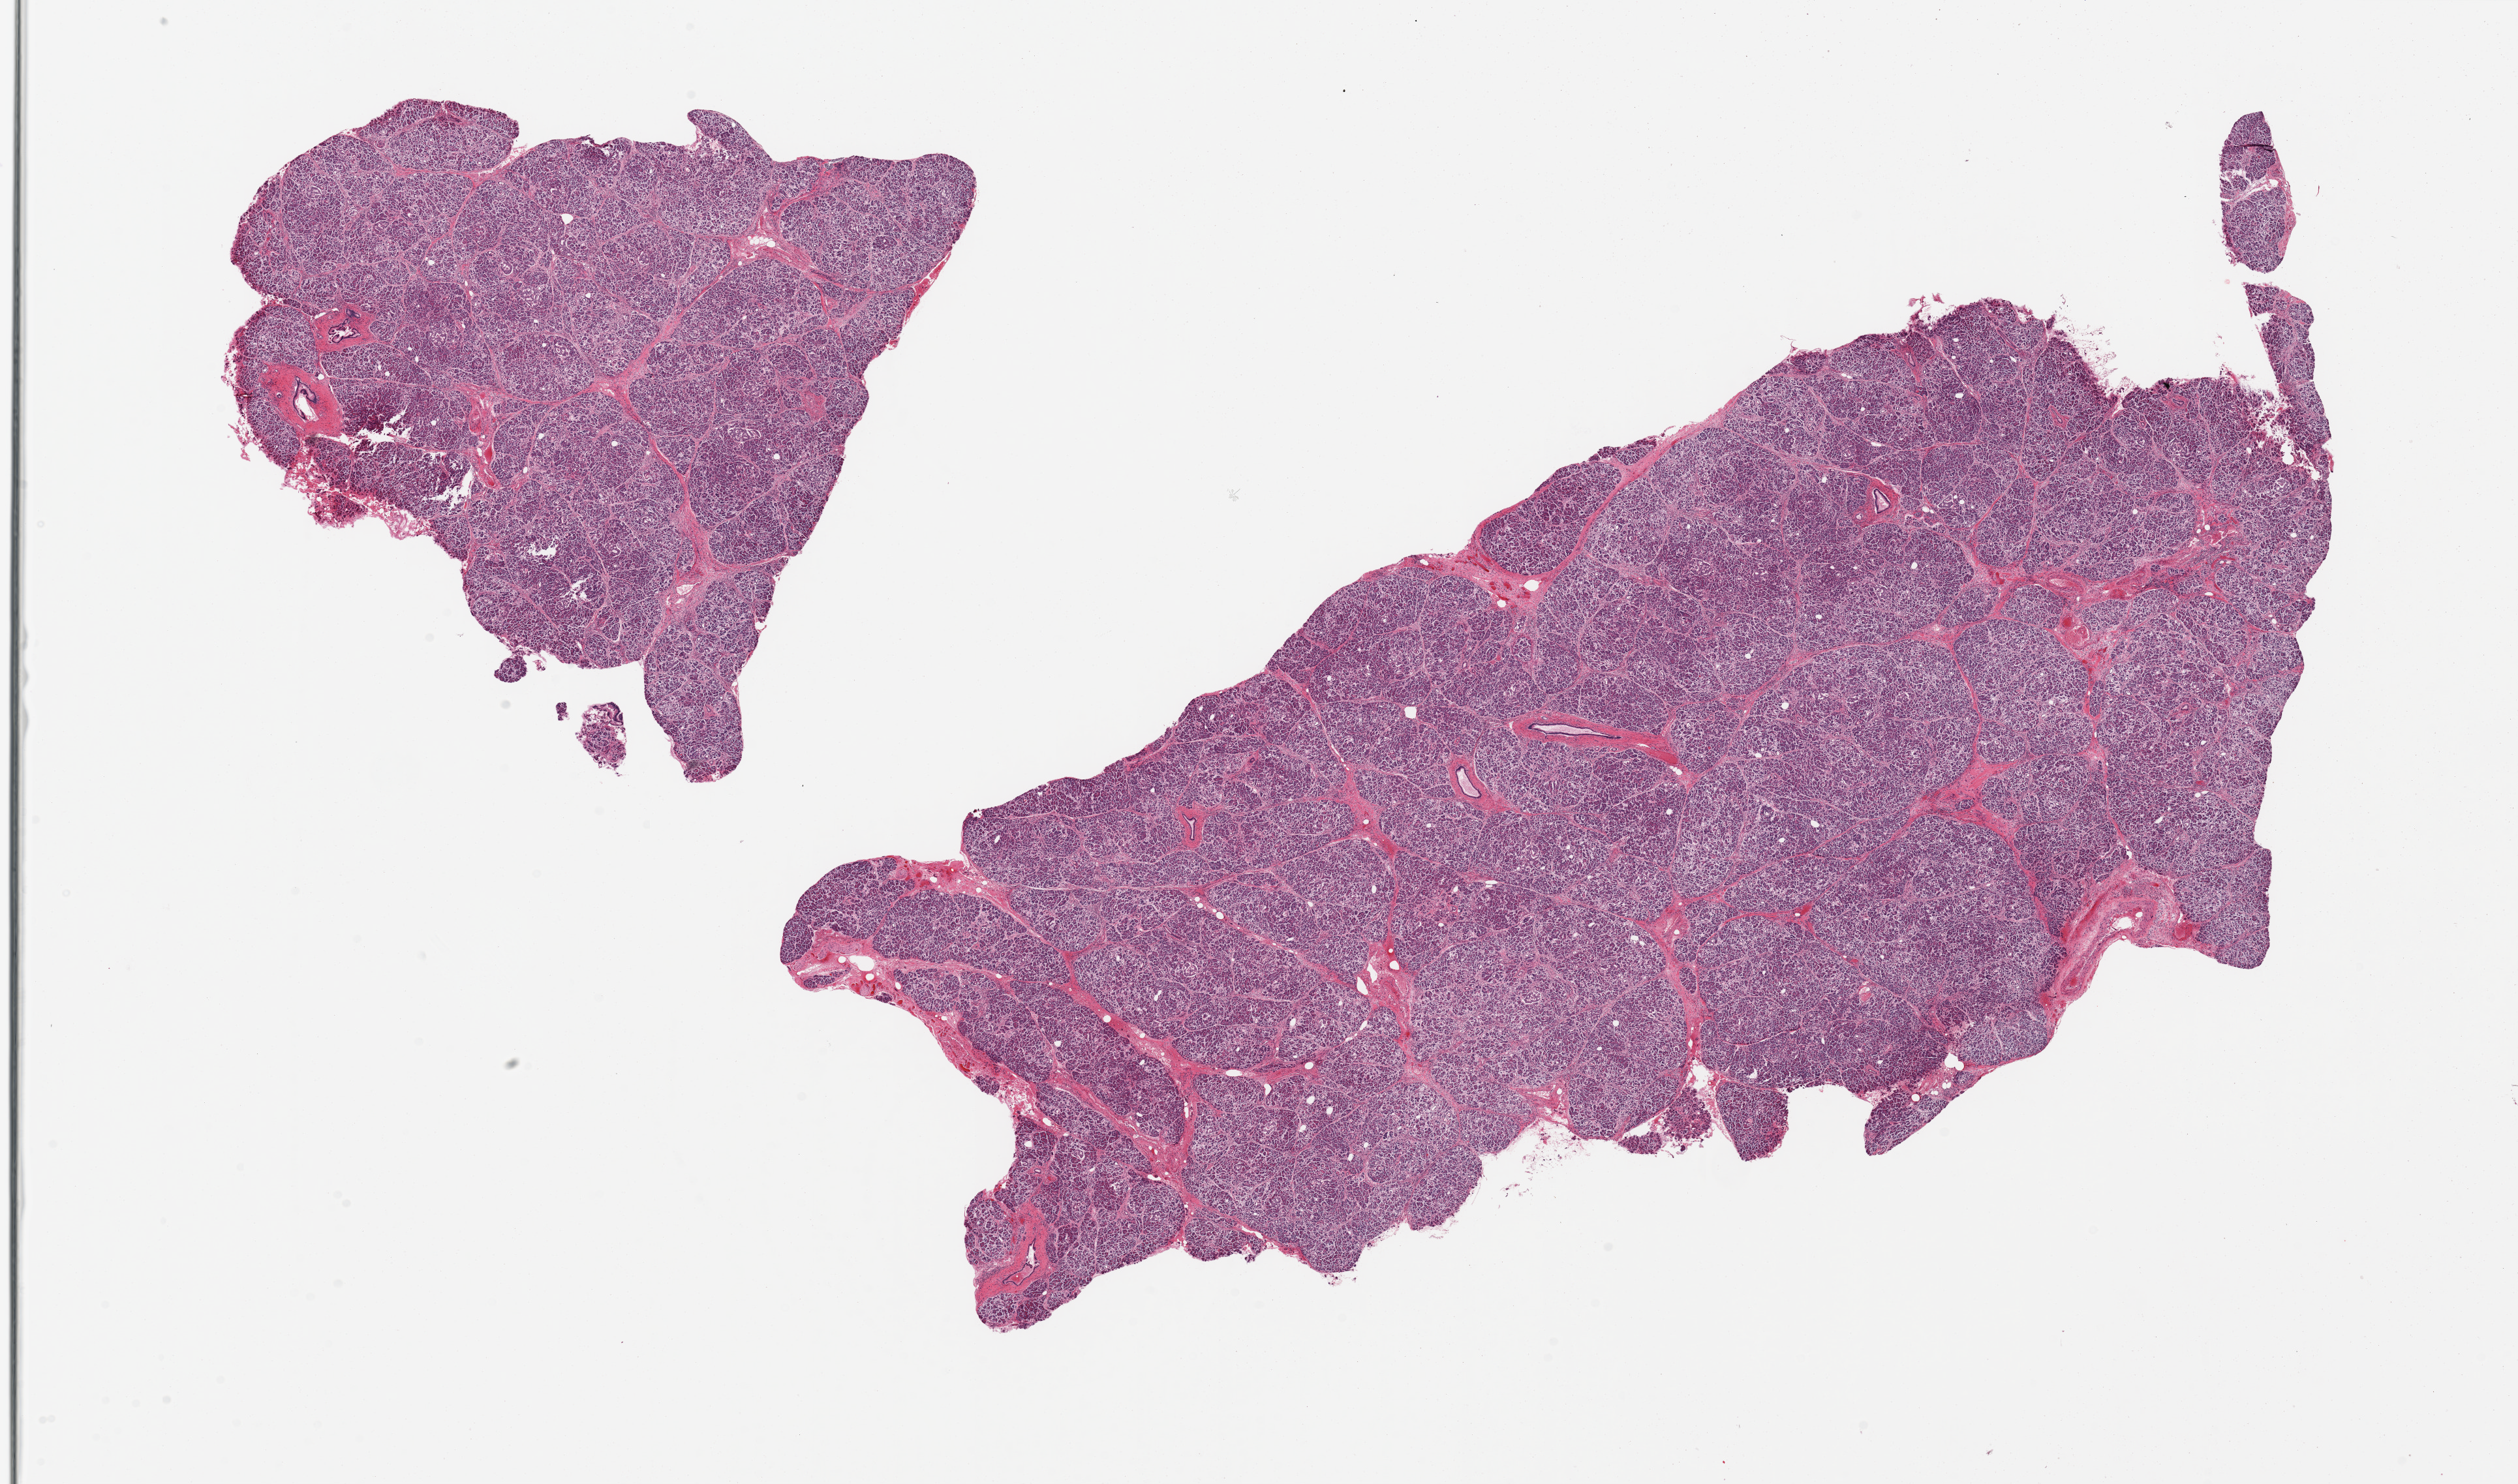
H&E whole-slide image — shown as a low-resolution overview of the whole scanned area (about 30.5 x 18.0 mm). PAXgene-fixed paraffin-embedded (PFPE) section. Section of pancreas (target tissue). Tissue donor sample. Donor sex: female.
Reviewer comment on this tissue sample: 2 pieces, moderately autolyzed, Islets still discernable.